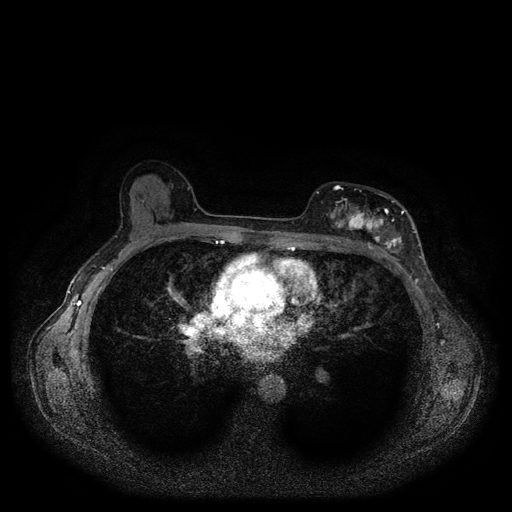
Breast MRI (dynamic contrast-enhanced, multi-phase), one axial slice; slice 62 of 116 in the series (ordered by position); dynamic contrast-enhanced series, time point 2 of 5 at this slice position (early post-contrast); 1.5 T; TE 2.6 ms, TR 5.3 ms; 2 mm slice thickness; 512 × 512 image matrix, field of view 350 × 350 mm. Female patient, age 51 years.
Outlined on this slice (semi-automatic segmentation, software-assisted and operator-edited):
- breast lesion (labelled 'tumour' in the annotation; benign lesions carry a separate 'benign' label): box from (x=324, y=193) to (x=394, y=246) px